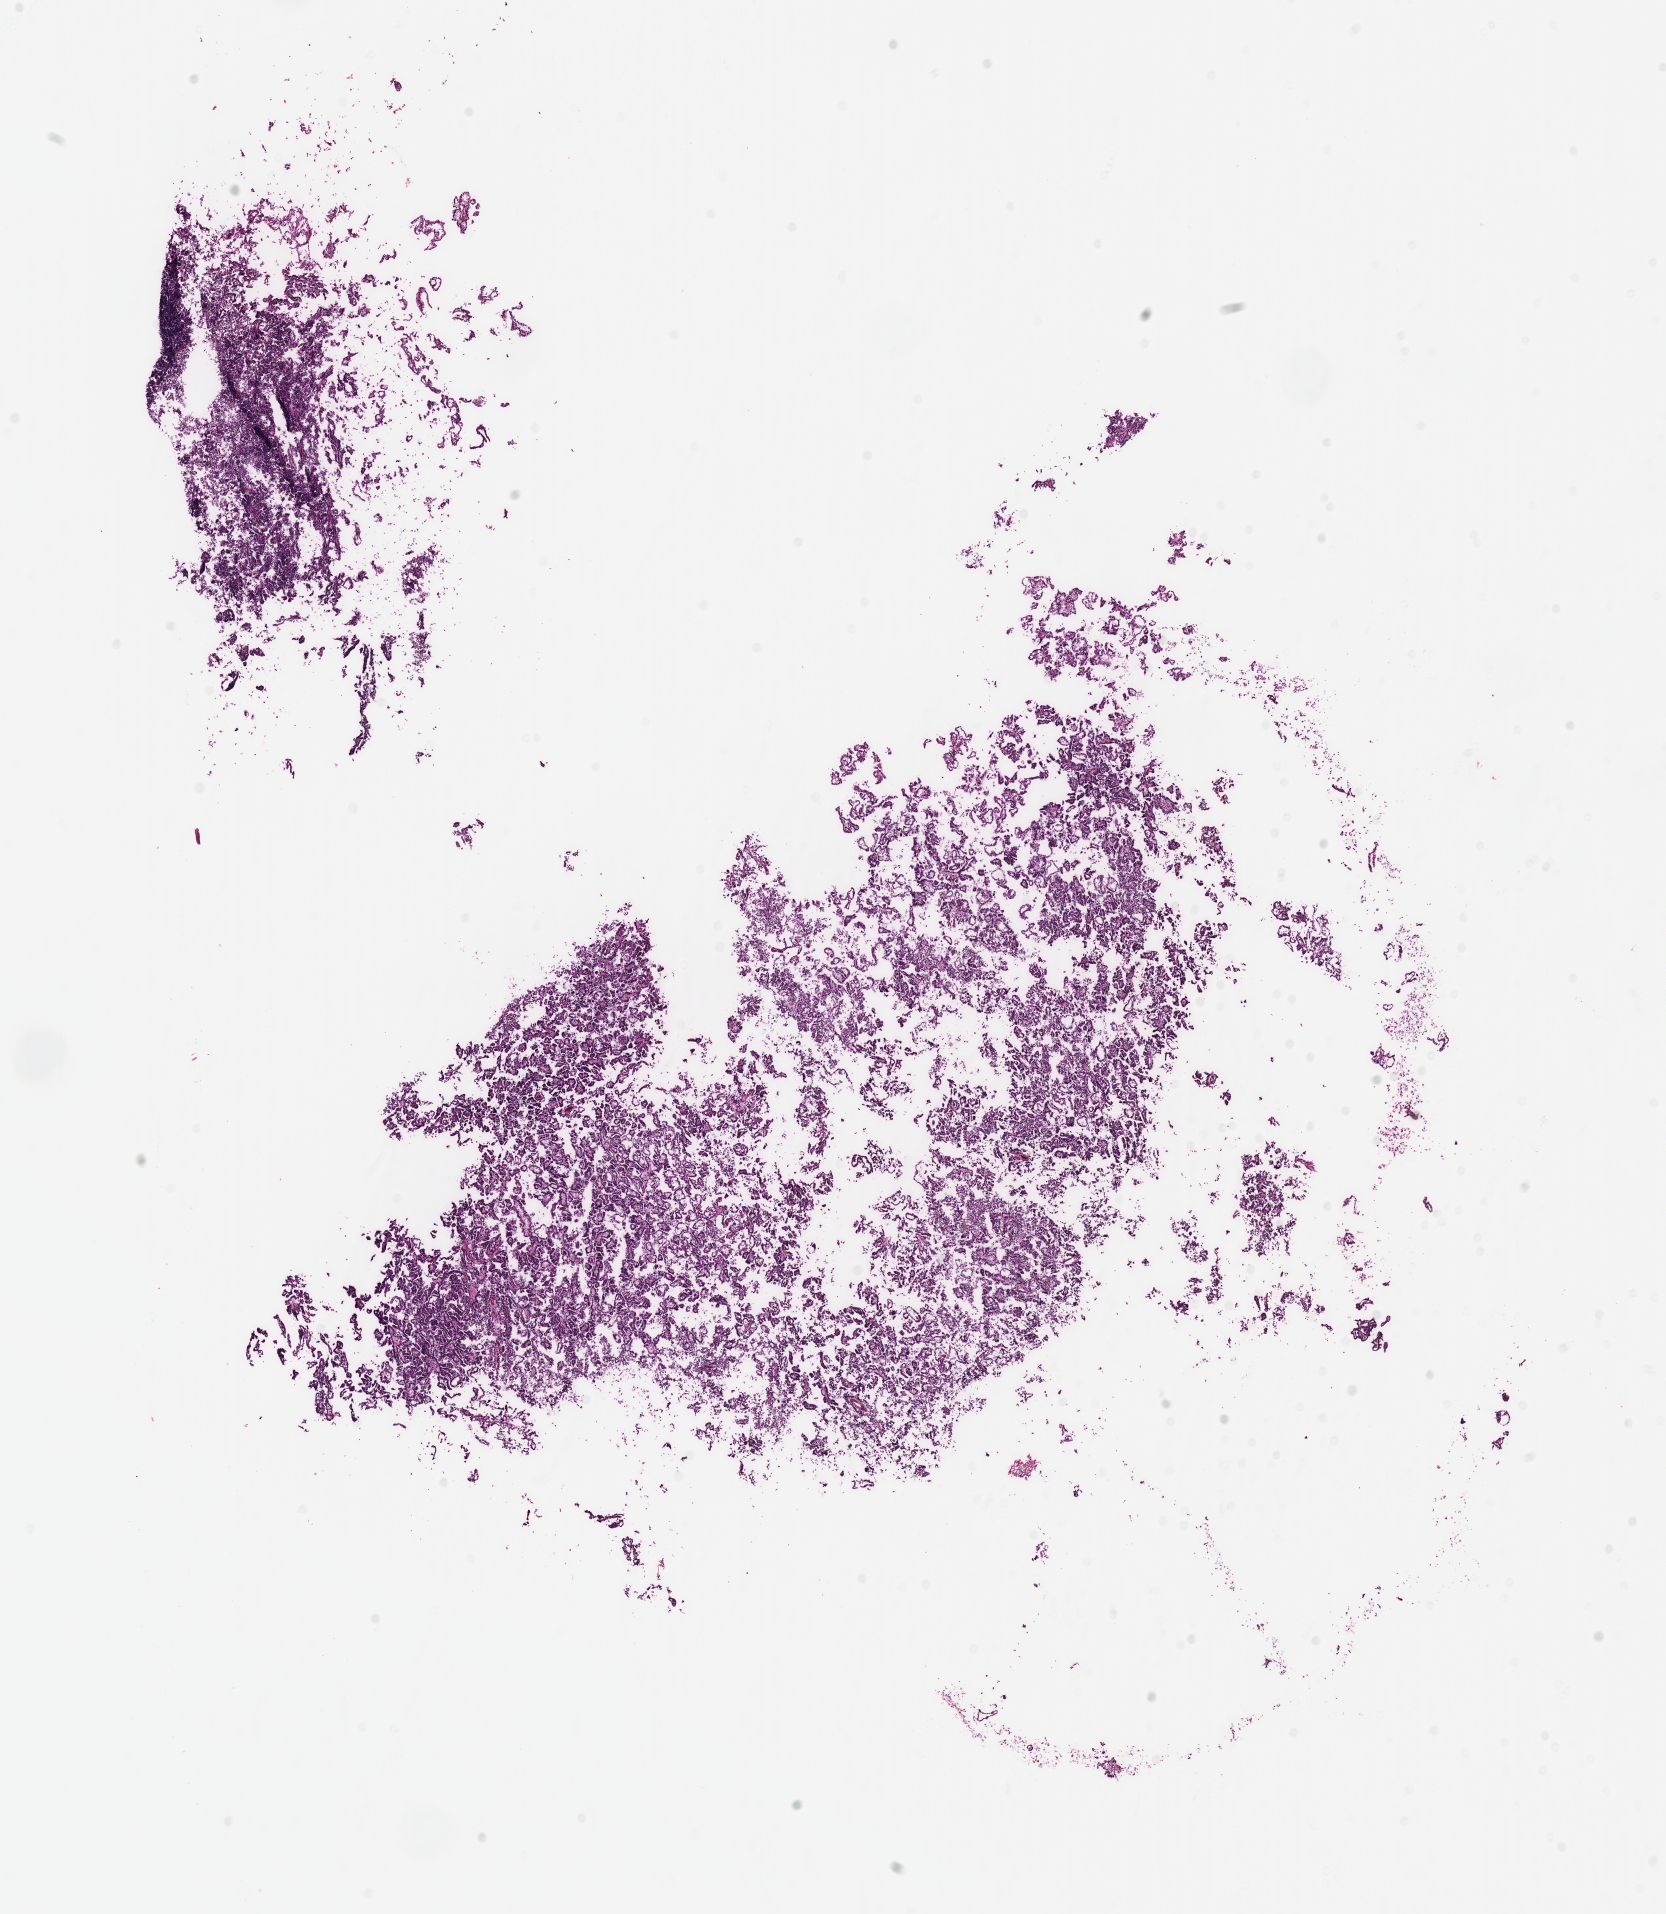
Whole-slide histology image, H&E — a low-resolution overview of the entire scanned area, about 13.1 x 15.1 mm (acquisition: 40x scan), frozen section from the top of the tissue portion, primary tumour sample from the kidney. Patient: male, age at initial diagnosis 60 years. Slide review estimates, as recorded: tumour cells 100%, tumour nuclei 90%, normal cells 0%, stromal cells 0%, necrosis 0%. Infiltration values recorded for this section: lymphocyte infiltration 0%, monocyte infiltration 5%, neutrophil infiltration 0%.
Laterality: right. Pathologic diagnosis: Papillary adenocarcinoma, NOS. TNM: T1b NX MX. AJCC pathologic stage: I (7th edition).